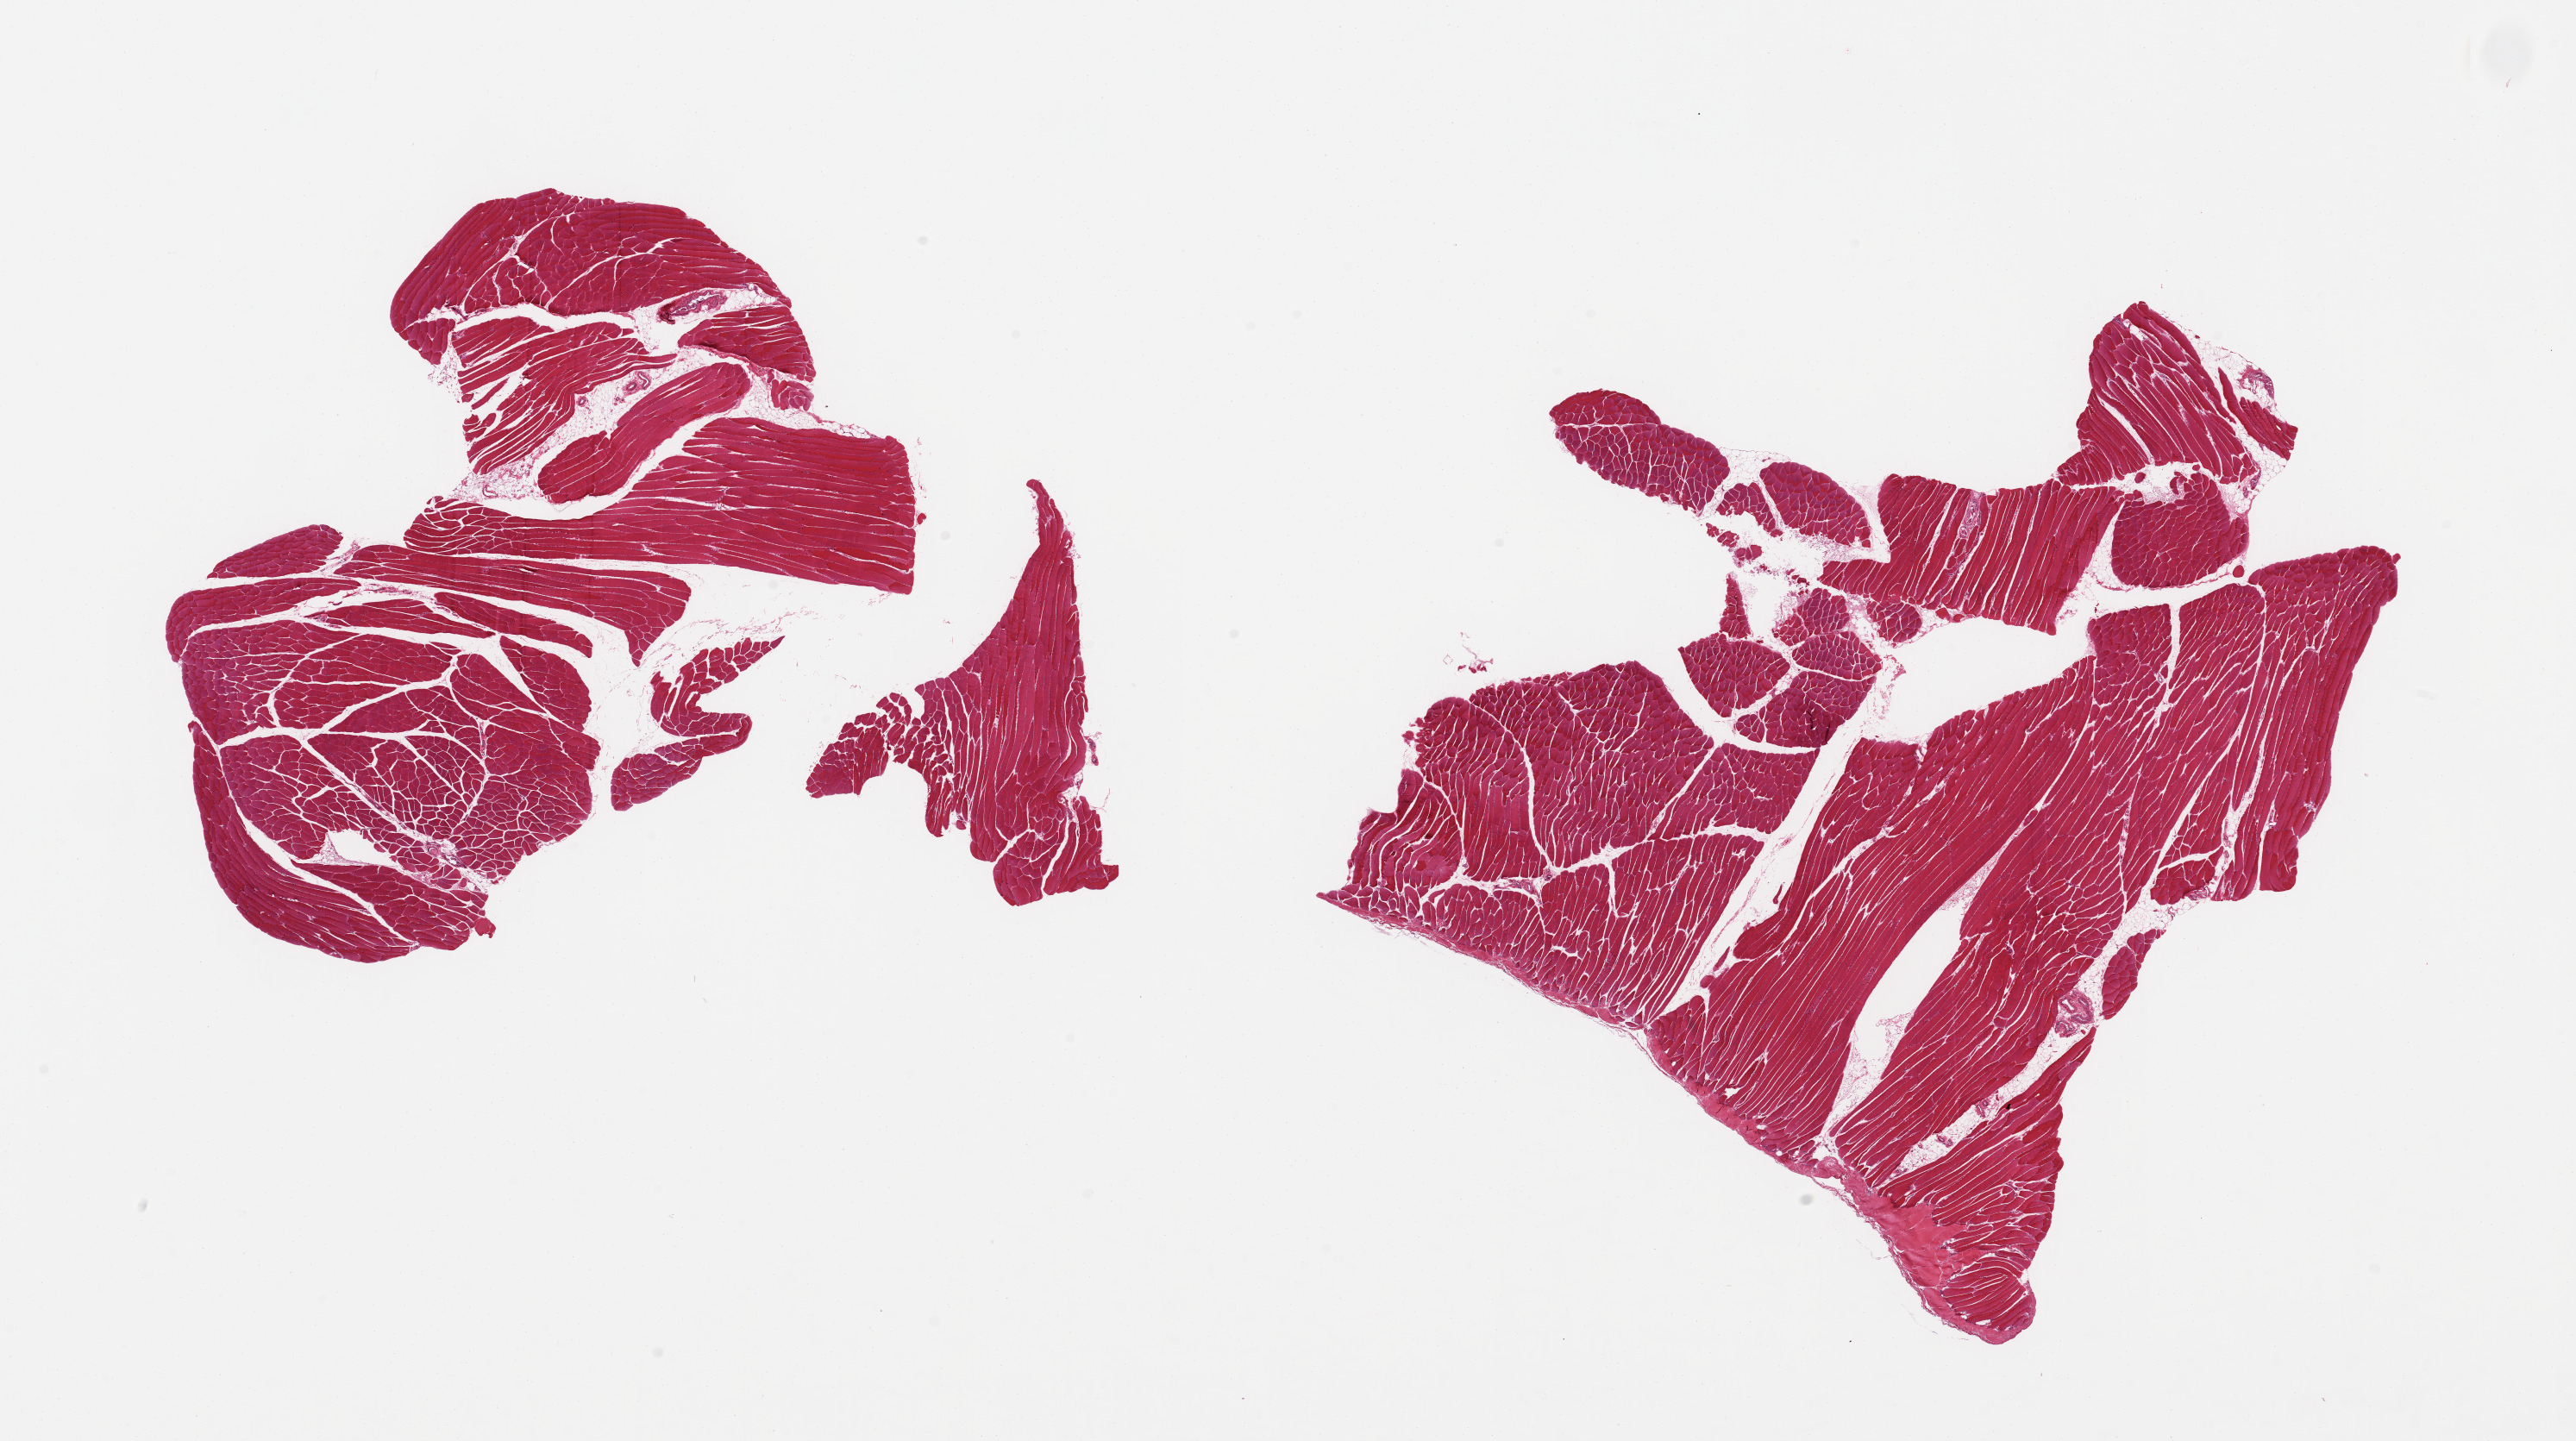
Whole-slide image, H&E stain — whole scanned area (about 23.6 x 13.2 mm) shown as a low-resolution overview; PAXgene-fixed paraffin-embedded (PFPE) section; target tissue: skeletal muscle; tissue donor sample. Donor: male.
Reviewer comment on this tissue sample: 2 pieces; skeletal muscle with up to ~5-10% internal fat, small portion of tendon.